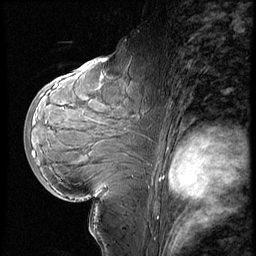
Breast MRI (dynamic contrast-enhanced), one sagittal slice; slice 35 of 60 in the series (ordered by position); 3 images stored at this slice position (order not interpretable as contrast timing); 1.5 T; TE 4.2 ms, TR 8.9 ms; 256 × 256 image matrix, field of view 200 × 200 mm. Patient: female, 29 years. From the clinical record (not read from this slice): setting: breast cancer imaged before/during neoadjuvant chemotherapy.
Outlined on this slice (semi-automatic segmentation, software-assisted and operator-edited):
- analysis volume of interest (the breast-tissue region the enhancement analysis was run in; not a lesion): bounding box (x1, y1, x2, y2) in pixels: (29, 57, 150, 200)
- tumour enhancement mask (voxels above the 140 % enhancement threshold inside the analysis volume of interest): (34, 85, 58, 158)